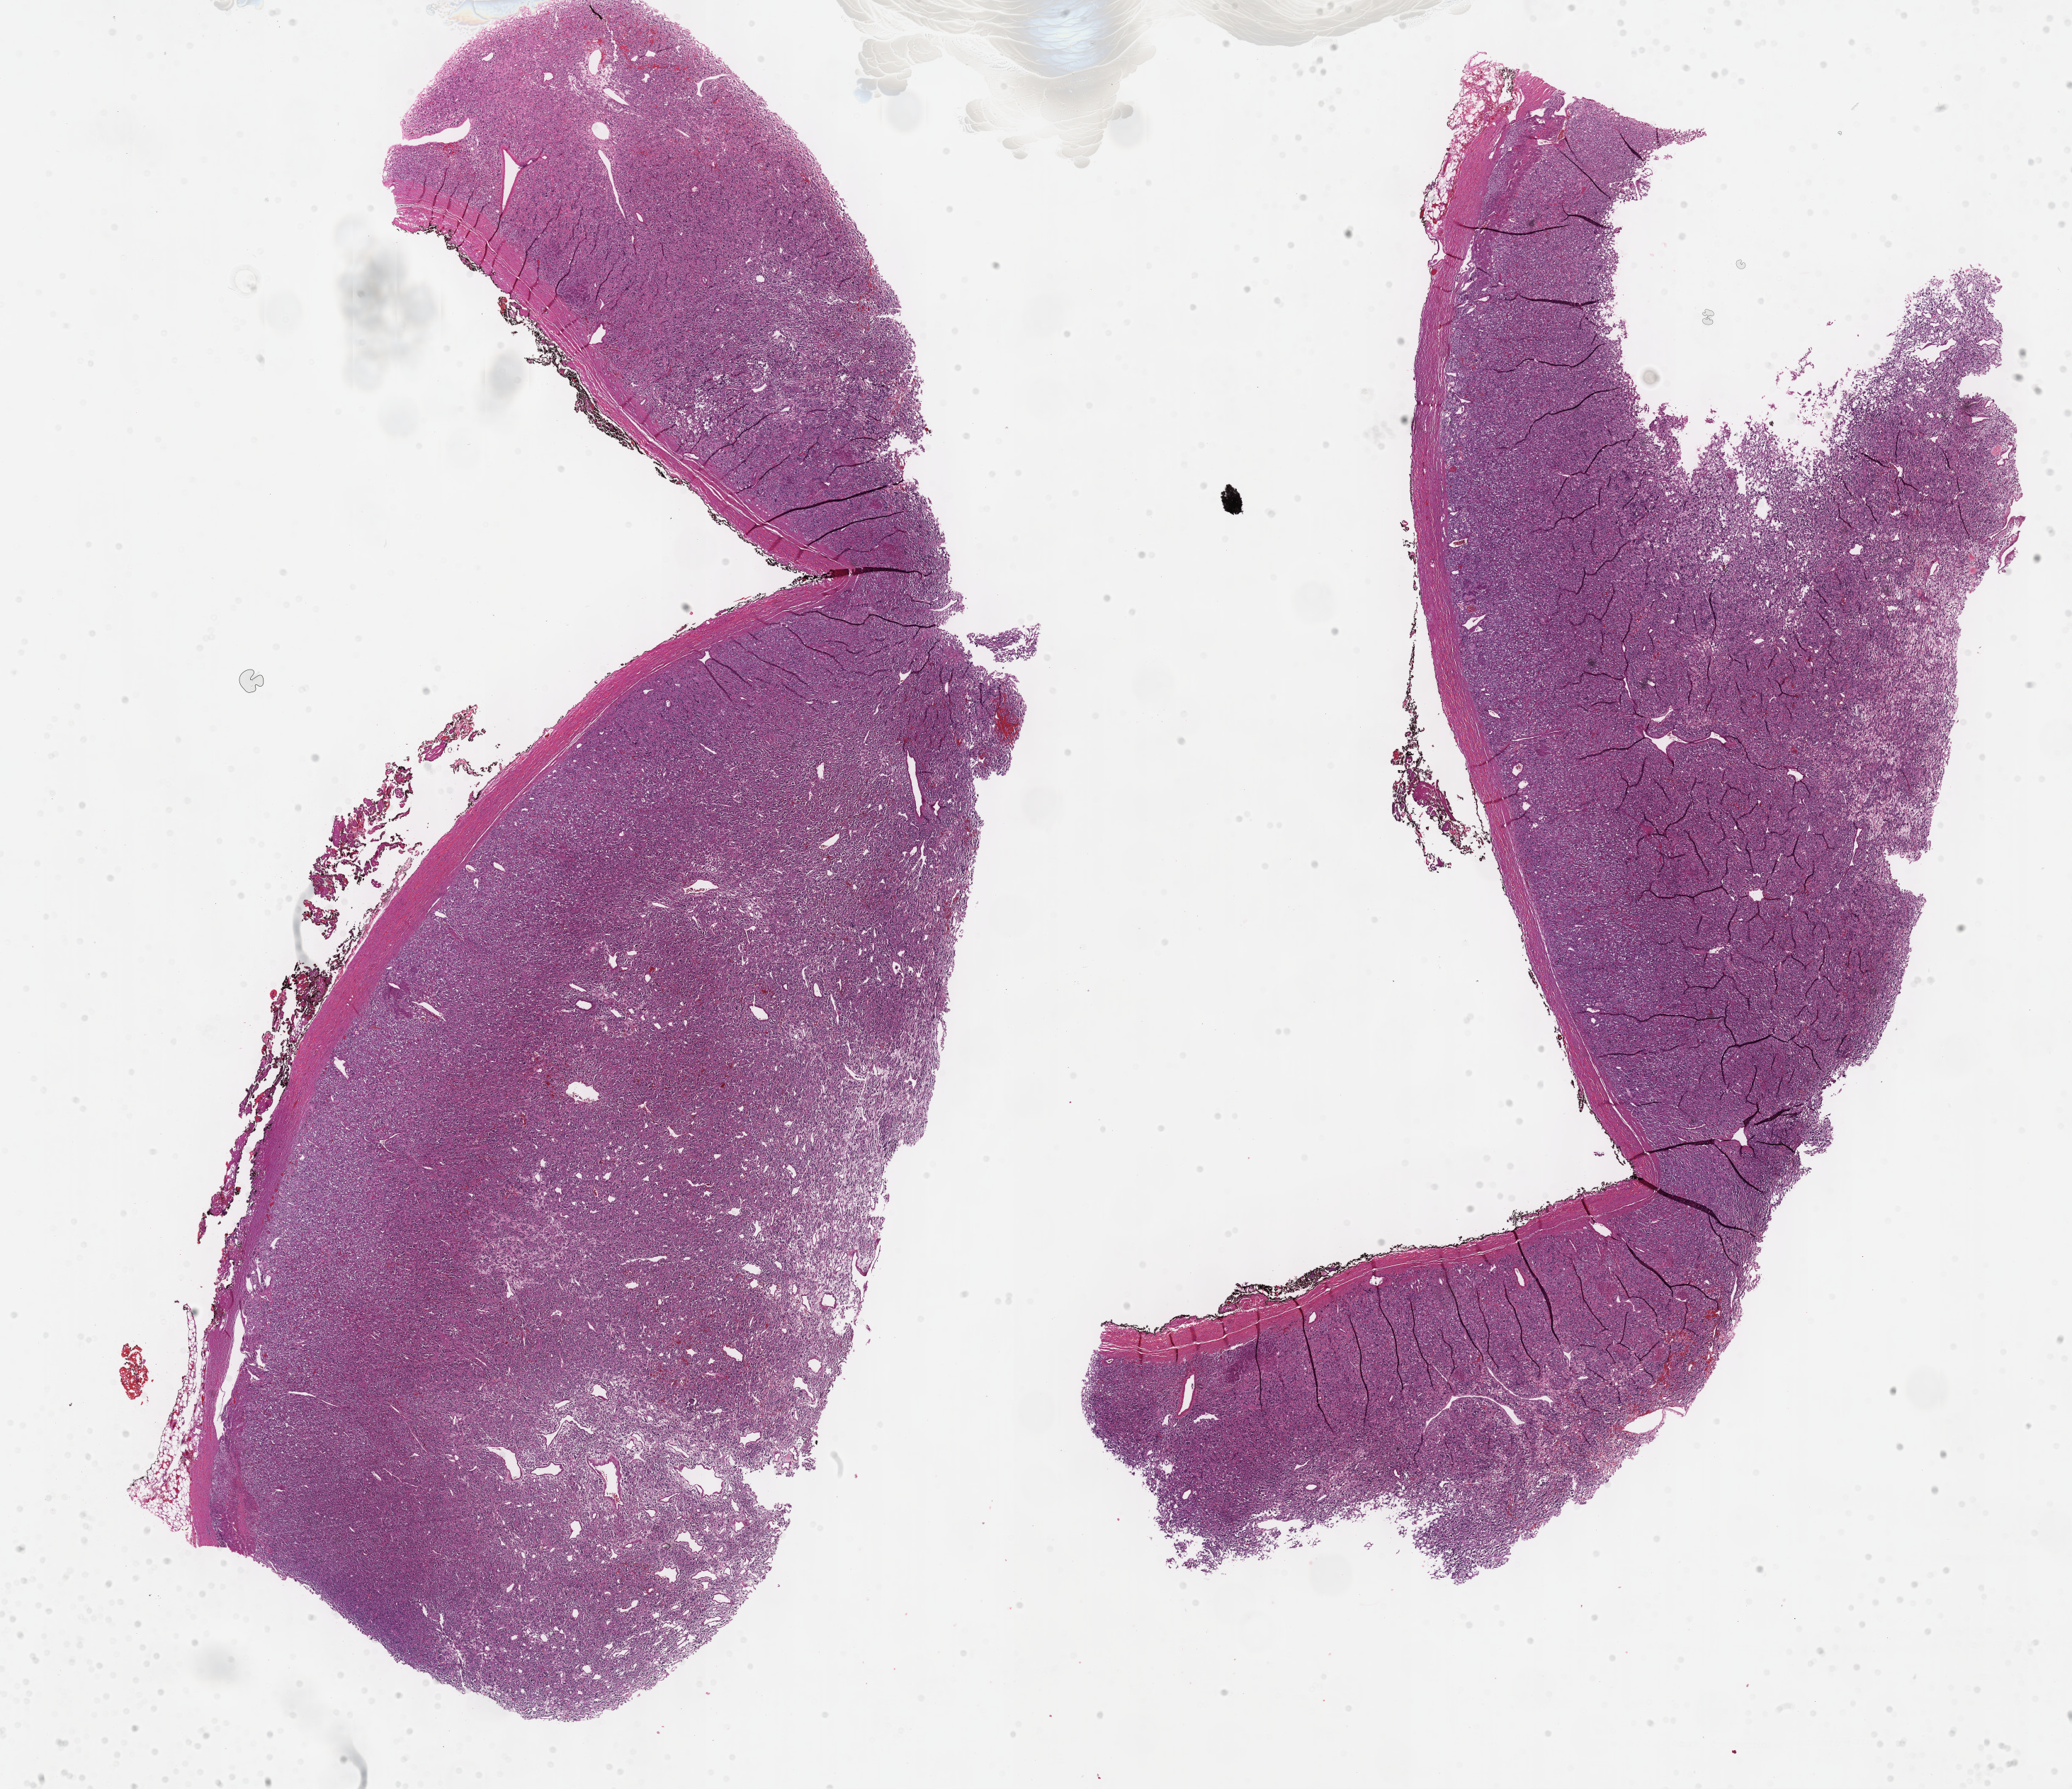
Digitized H&E-stained tissue section (whole slide) — a low-resolution overview of the entire scanned area, about 23.7 x 20.4 mm, FFPE section, adrenal gland, primary tumour sample. Patient: male, age at initial diagnosis 31 years.
- pathologic diagnosis: Pheochromocytoma, NOS